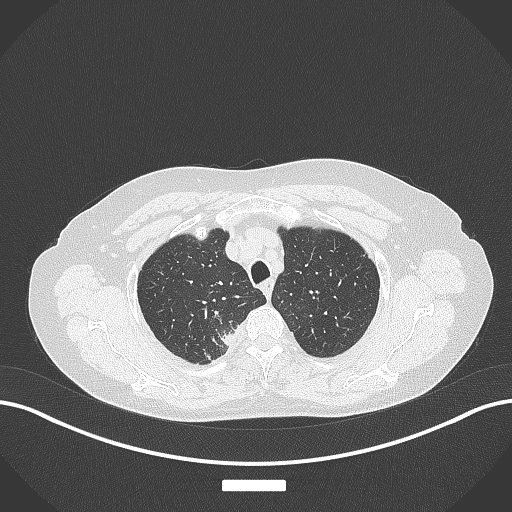
Chest CT, one axial slice. Slice 324 of 357 in the series (ordered by position). Lung window (W 1500 / L -600 HU). 512 × 512 image matrix. Patient: female, 62 years. Case-level facts recorded for this patient, not image findings: clinical TNM (as recorded): T1c N1 M0.
Annotated regions visible in this slice (bounding box drawn by a radiologist):
- lung tumour (recorded histology: squamous cell carcinoma): bounding box [x1, y1, x2, y2] px = [219, 328, 243, 353]